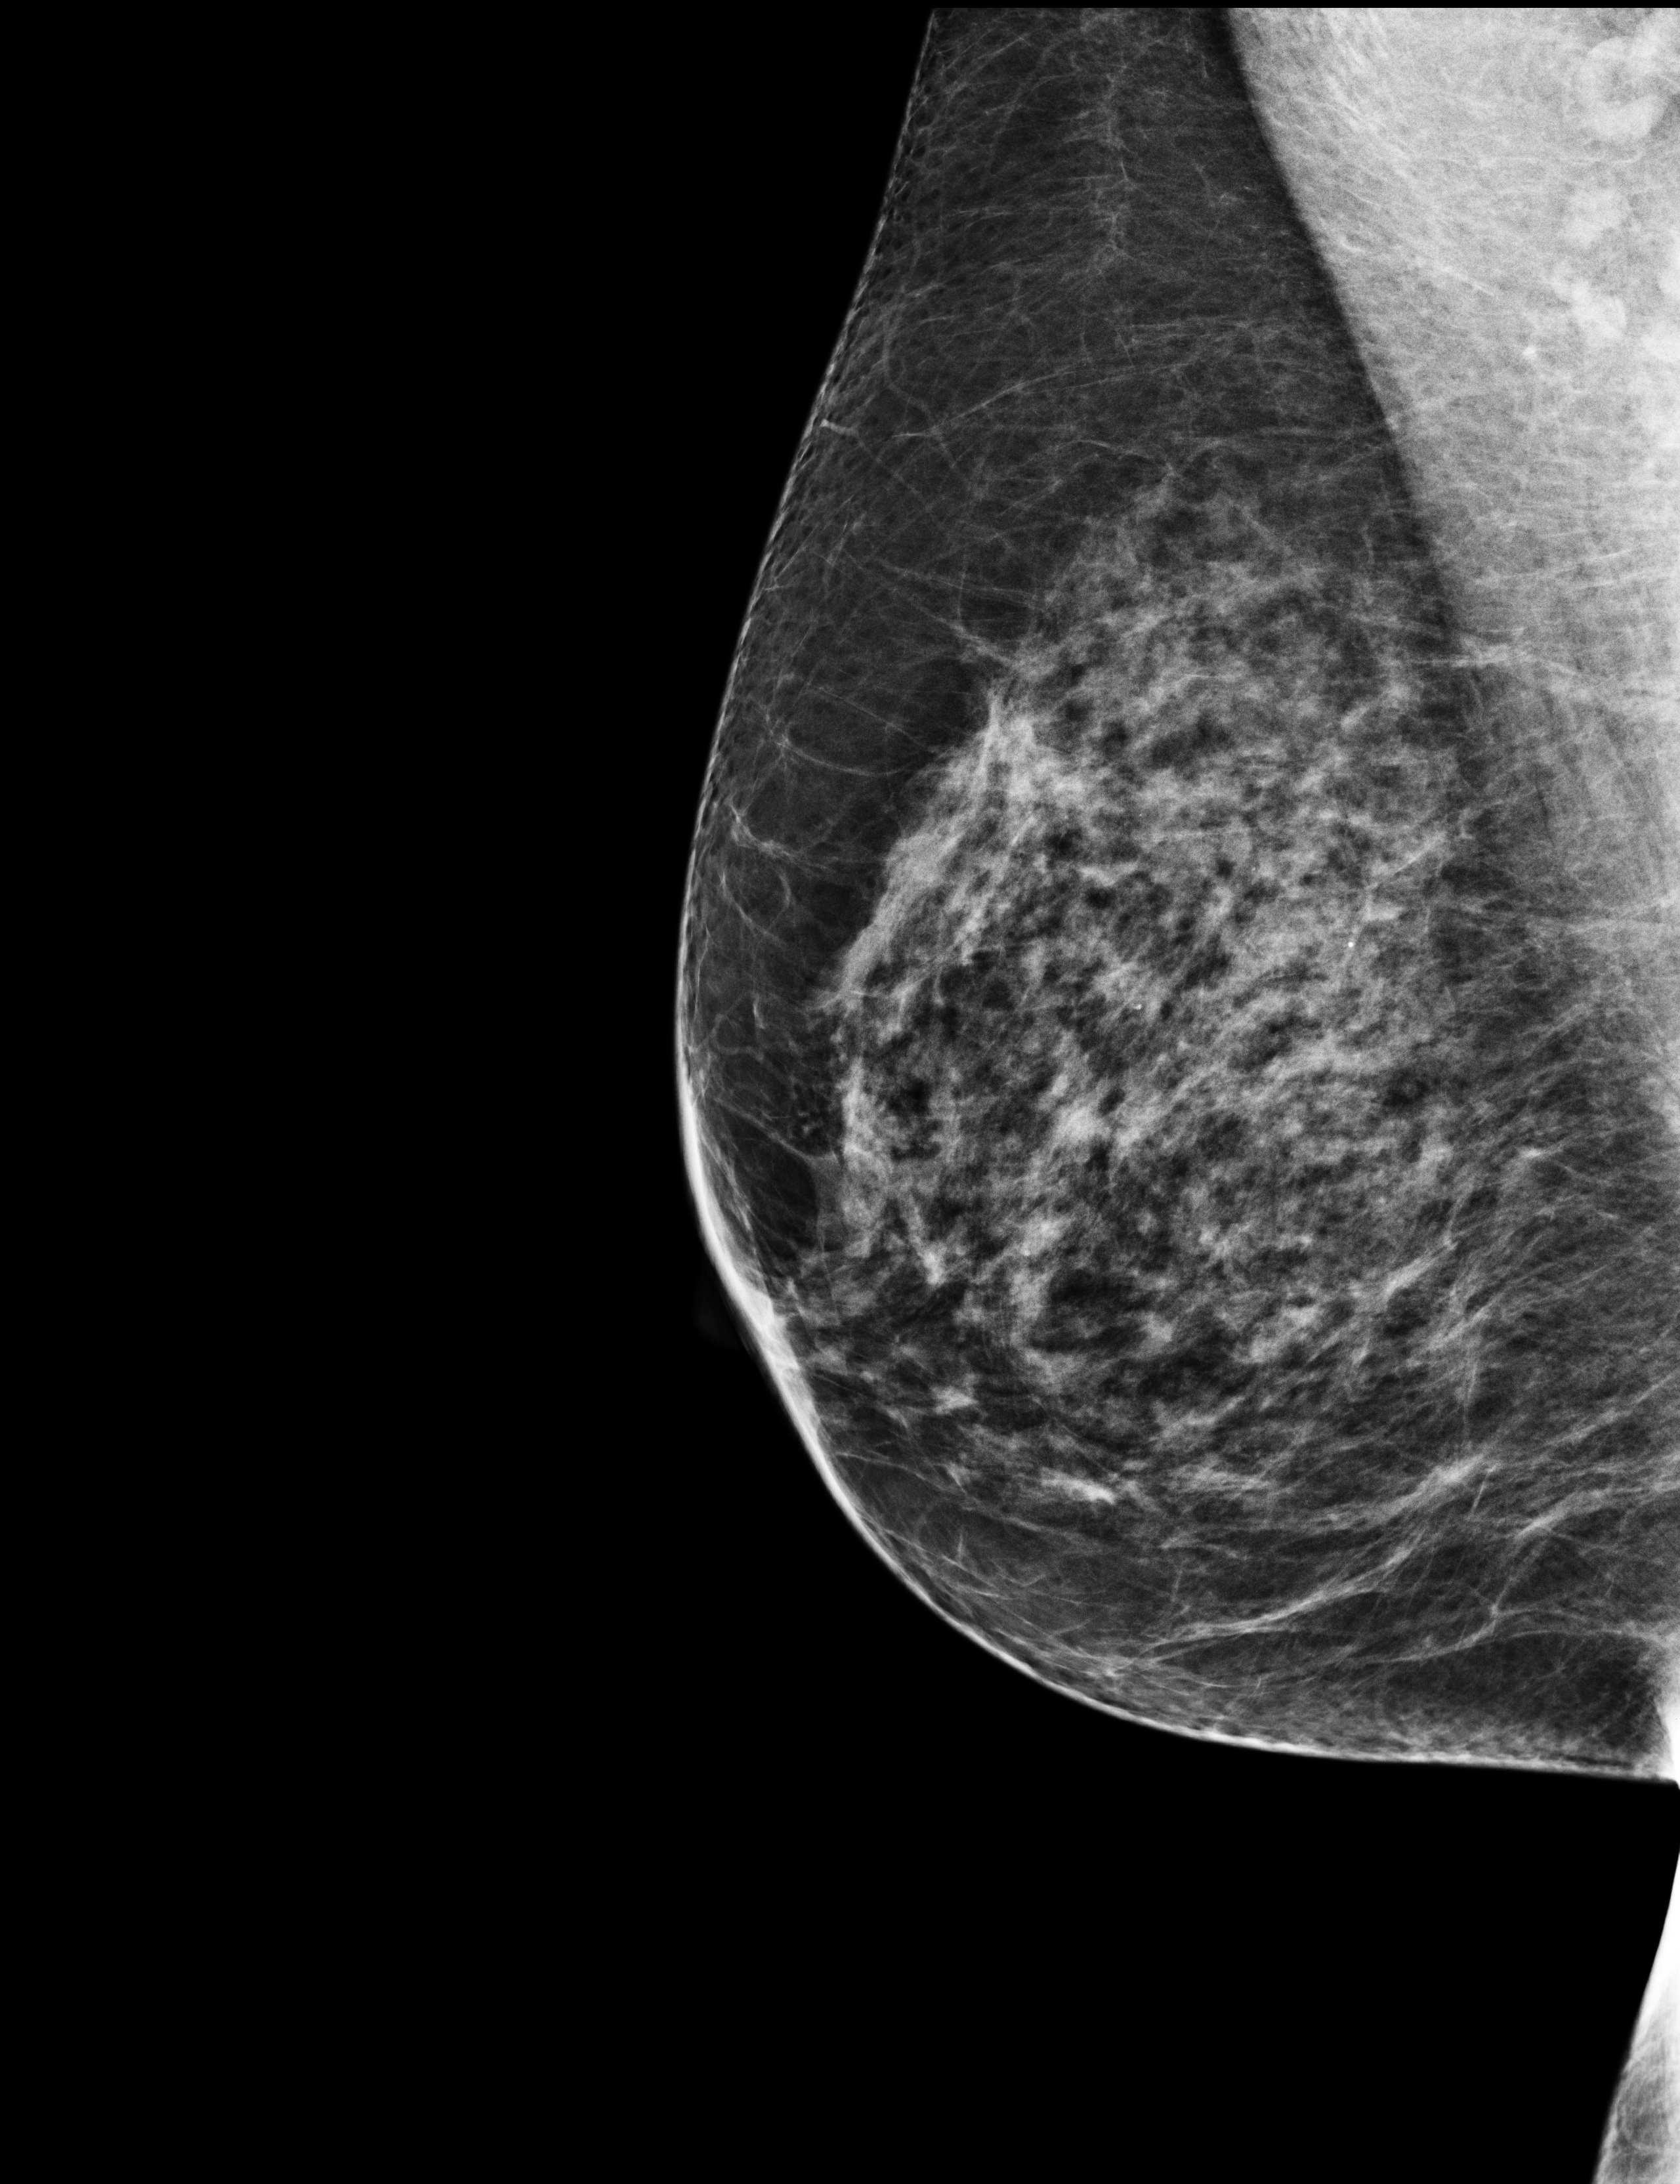
Full-field digital mammogram (FFDM), right breast, medio-lateral oblique projection, annual screening mammography examination. Female patient, age 60 years.
Final BI-RADS assessment for this screening round (tomosynthesis exam, both breasts): category 1.